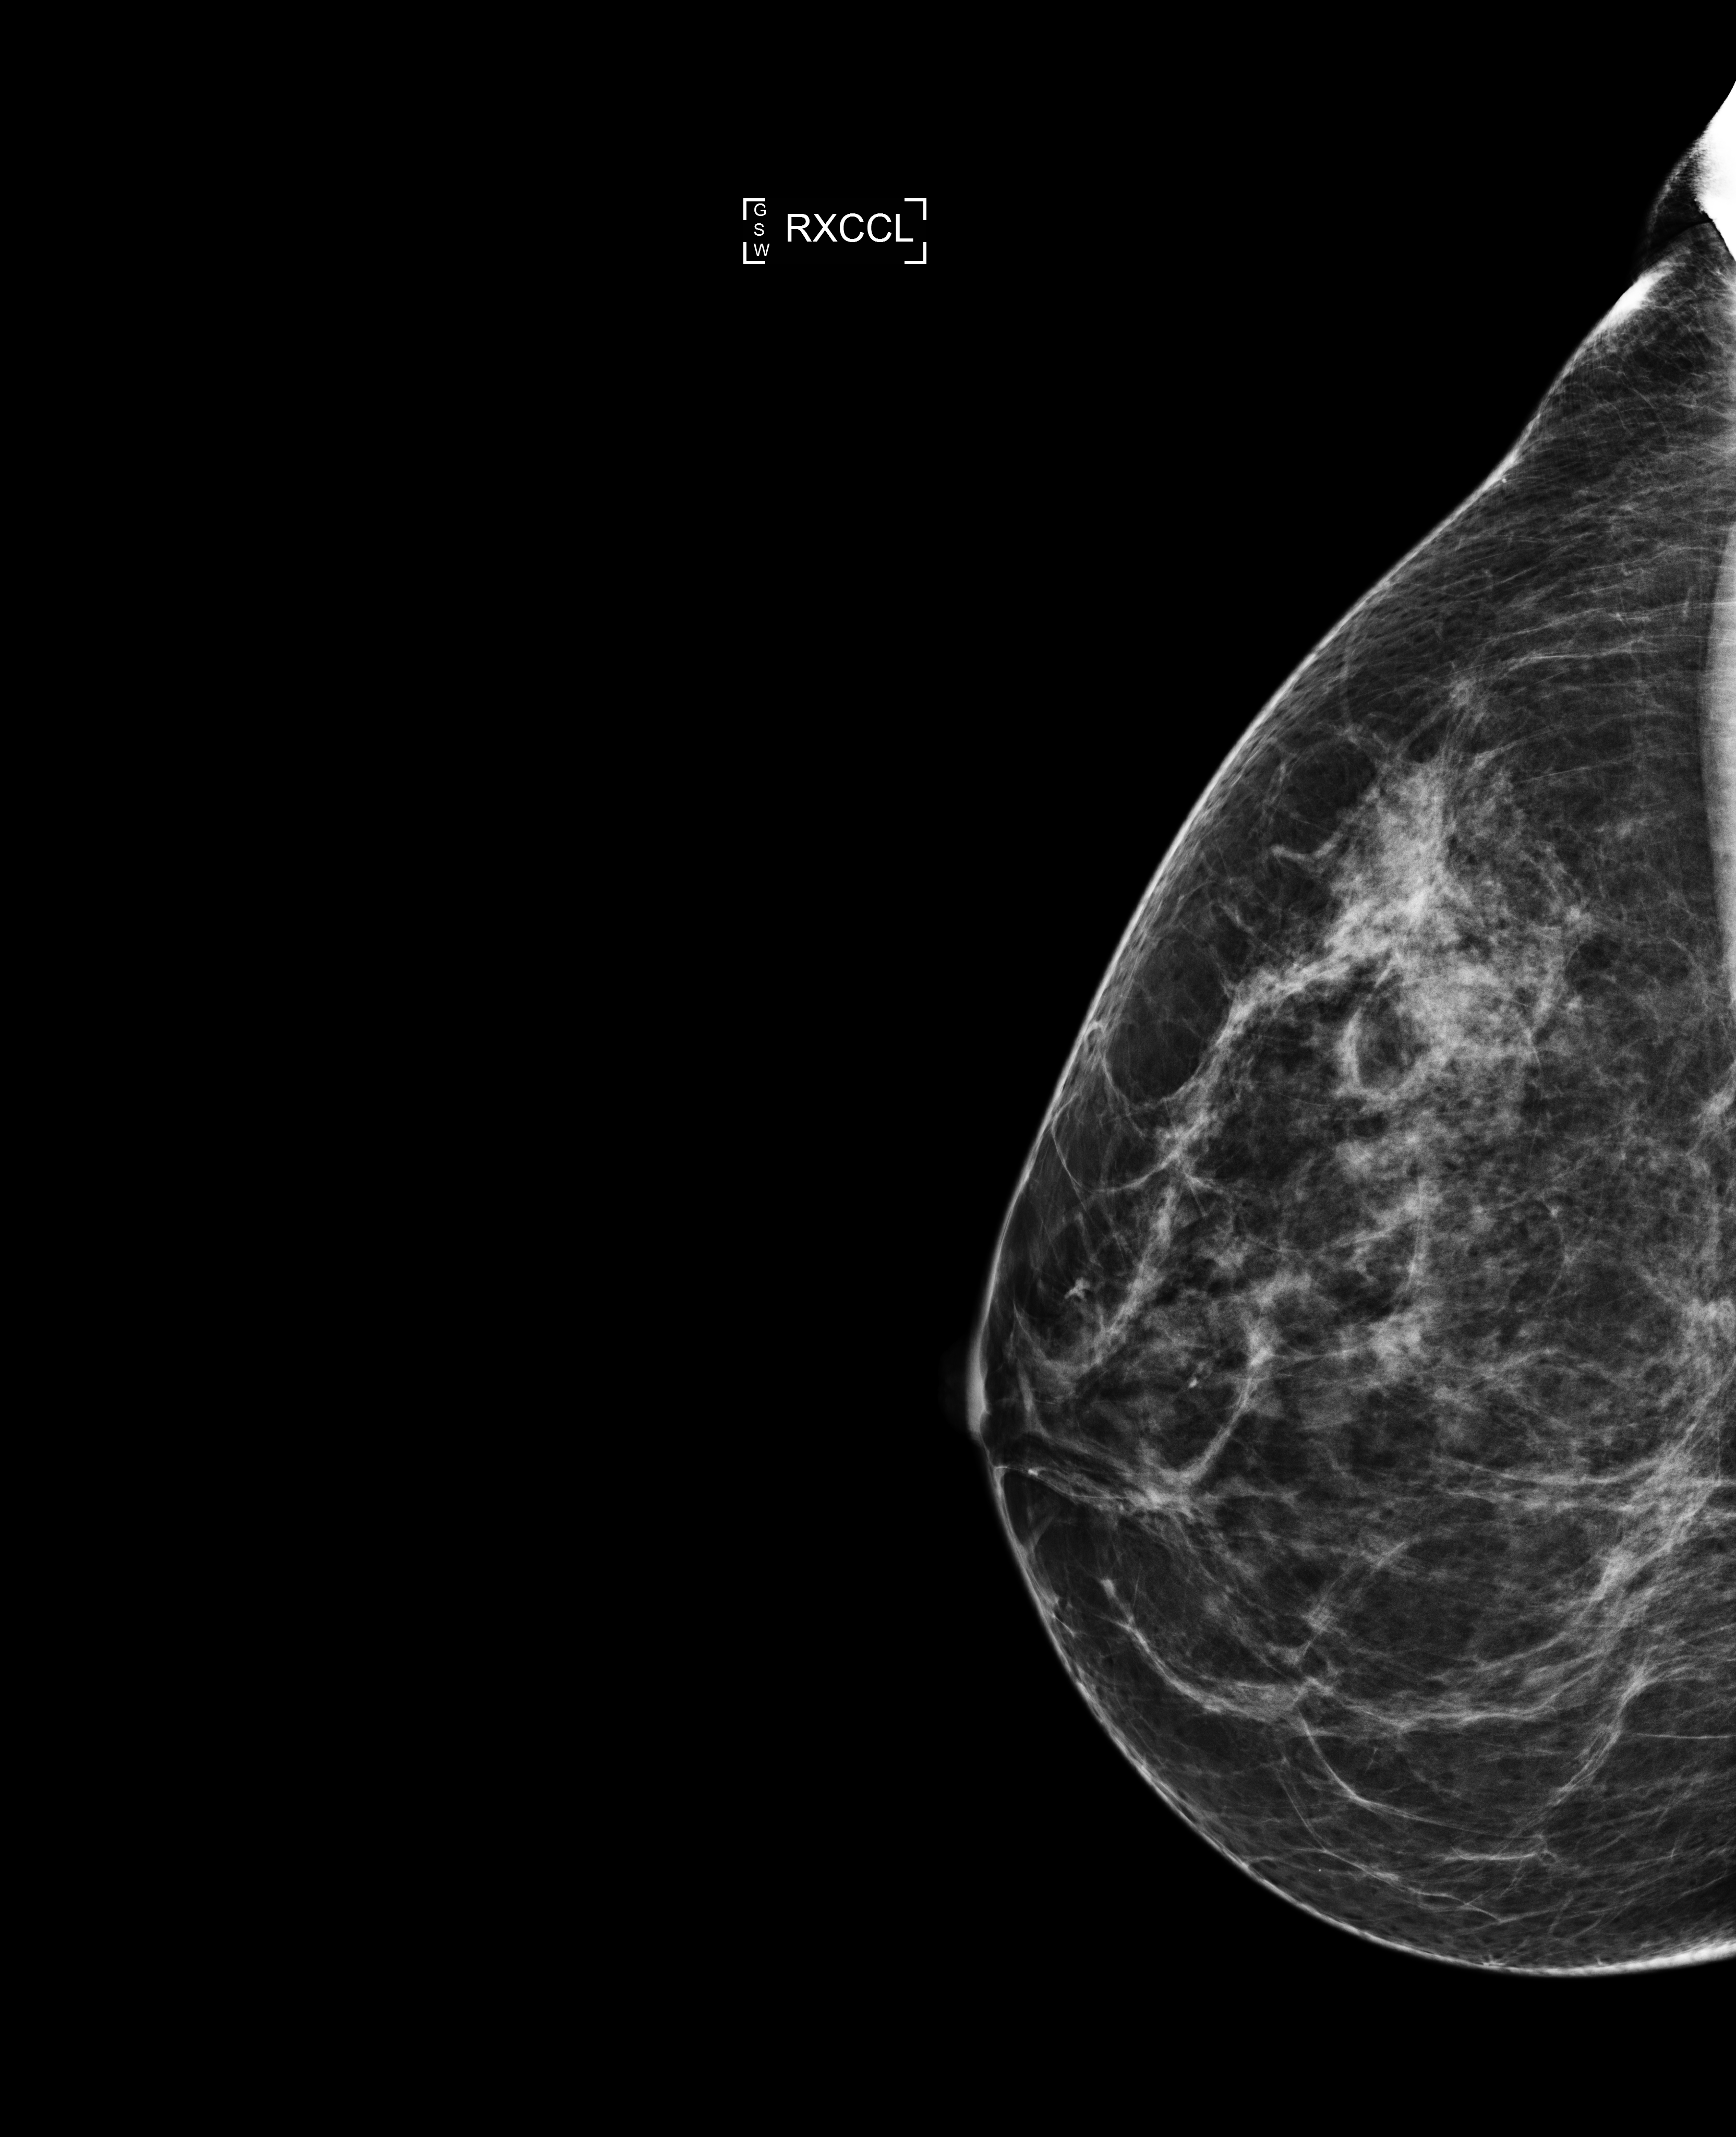
Full-field digital mammogram (FFDM); right breast; laterally exaggerated craniocaudal (XCCL) view; screening examination; system: Selenia Dimensions. Patient: female, 51 years.
Final BI-RADS category for the screening round (tomosynthesis exam, both breasts): category 1.